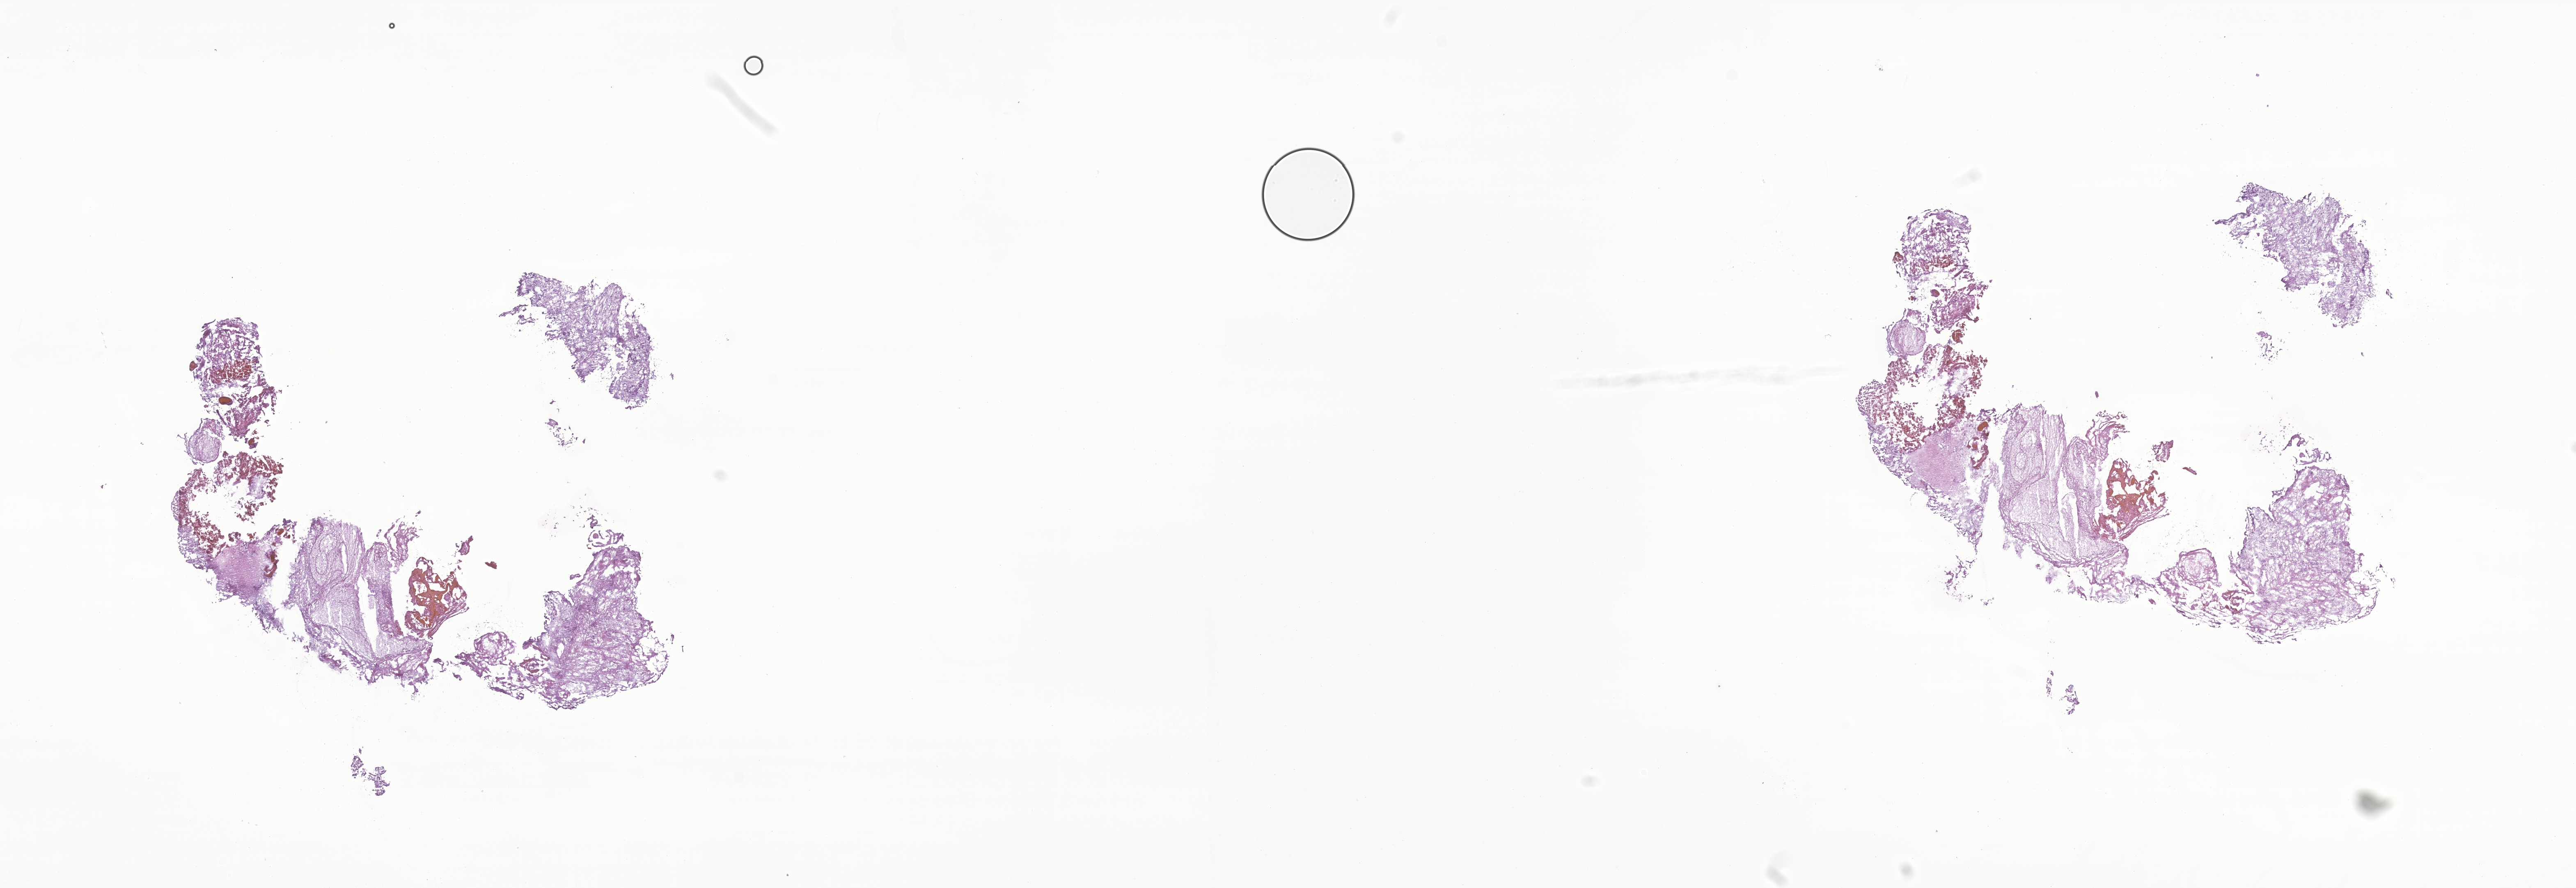
Digitized hematoxylin and eosin (H&E)-stained section of tumor tissue from the brain — whole scanned area (about 26.5 x 9.1 mm) shown as a low-resolution overview, frozen section (OCT-embedded). Patient female; age 114 months (9 years 6 months).
Diagnosis: Pilocytic astrocytoma.